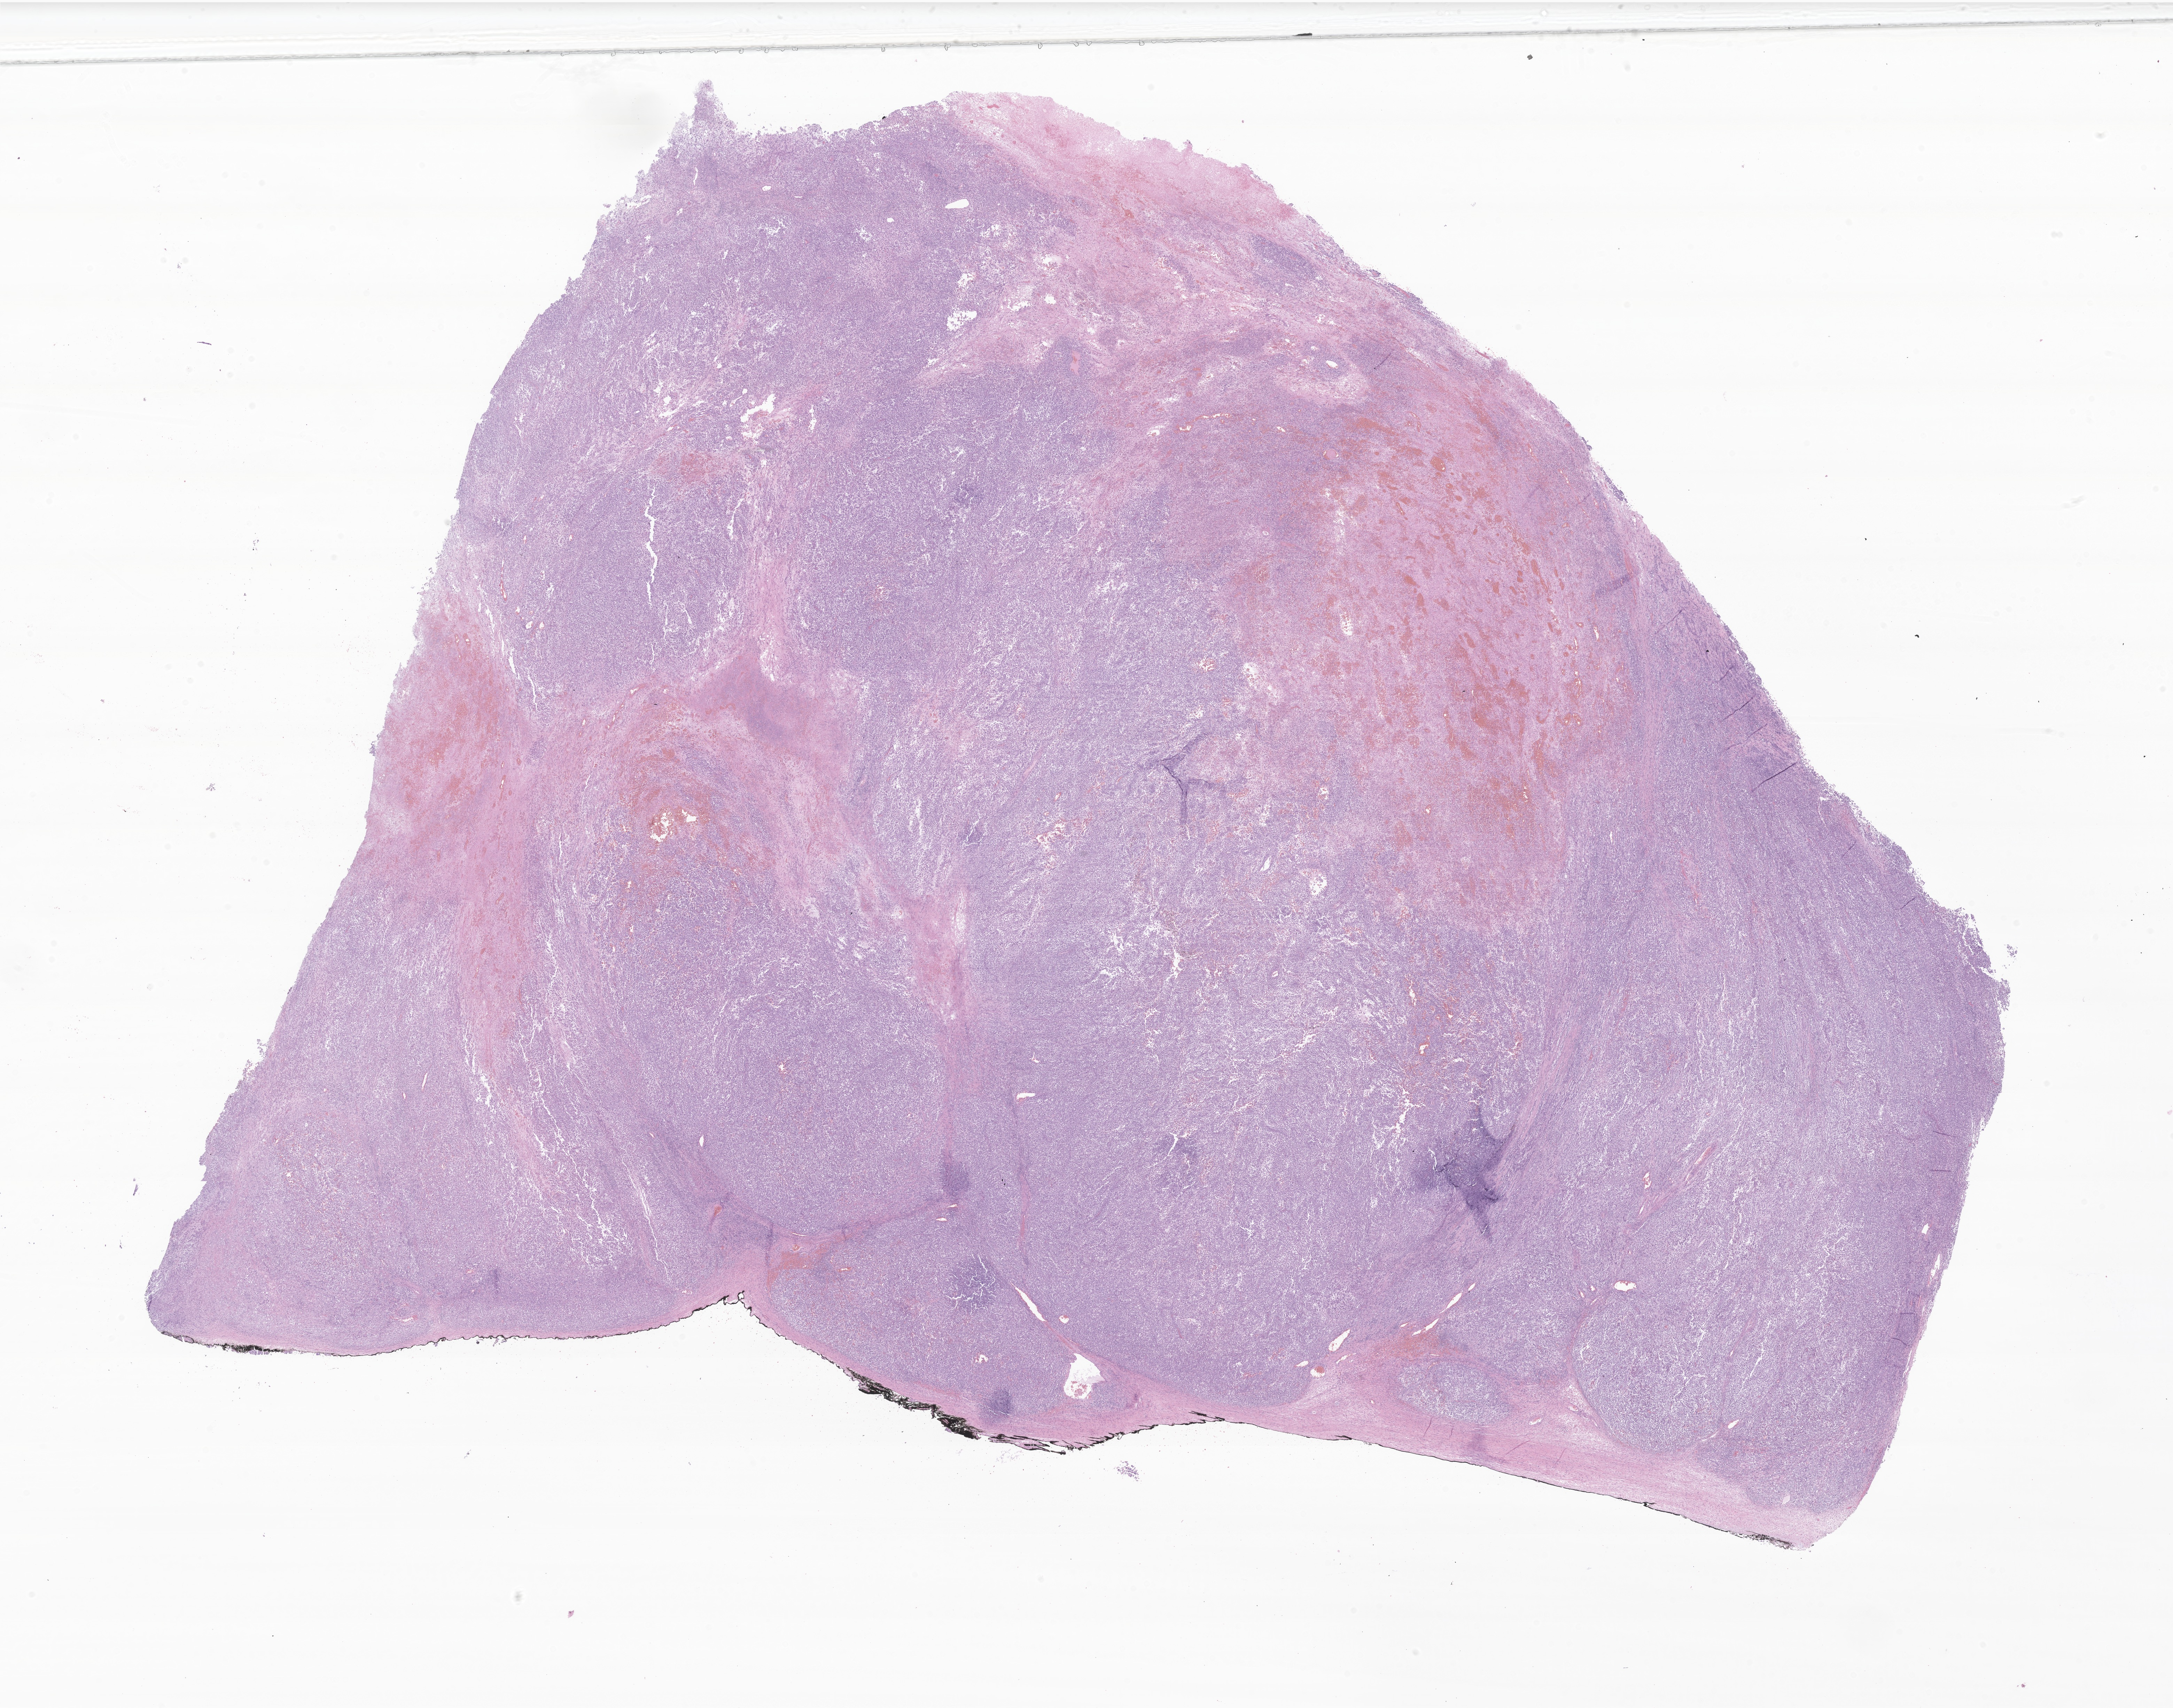
Digitized H&E-stained section of tumor tissue from the ovary — shown as a low-resolution overview of the whole scanned area (about 26.3 x 20.7 mm); FFPE section. Patient female; age 190 months (15 years 10 months).
Diagnosis: Small cell carcinoma, NOS.